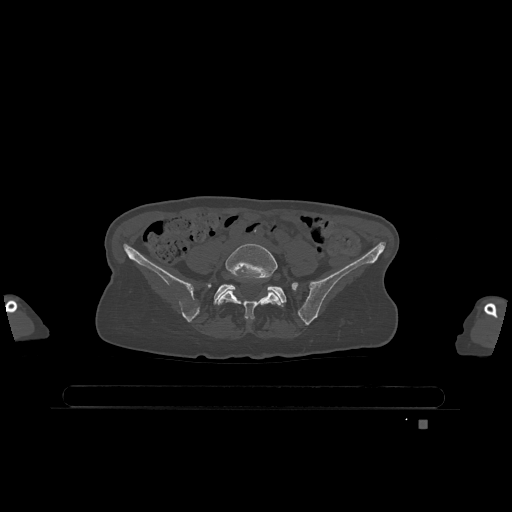
CT including the spine, one axial slice; bone window (W 1800 / L 400 HU); 0.5 mm slice thickness; 512 × 512 image matrix, field of view 500 × 500 mm. Female patient, age 74 years. Case-level facts recorded for this patient, not image findings: primary cancer: lung; vertebrae with lytic lesions (as recorded): T1, T4, T5, T6, L4, L5.
Outlined on this slice (semi-automatically segmented with operator editing):
- L5 vertebra: bounding box [x1, y1, x2, y2] px = [217, 243, 282, 320]